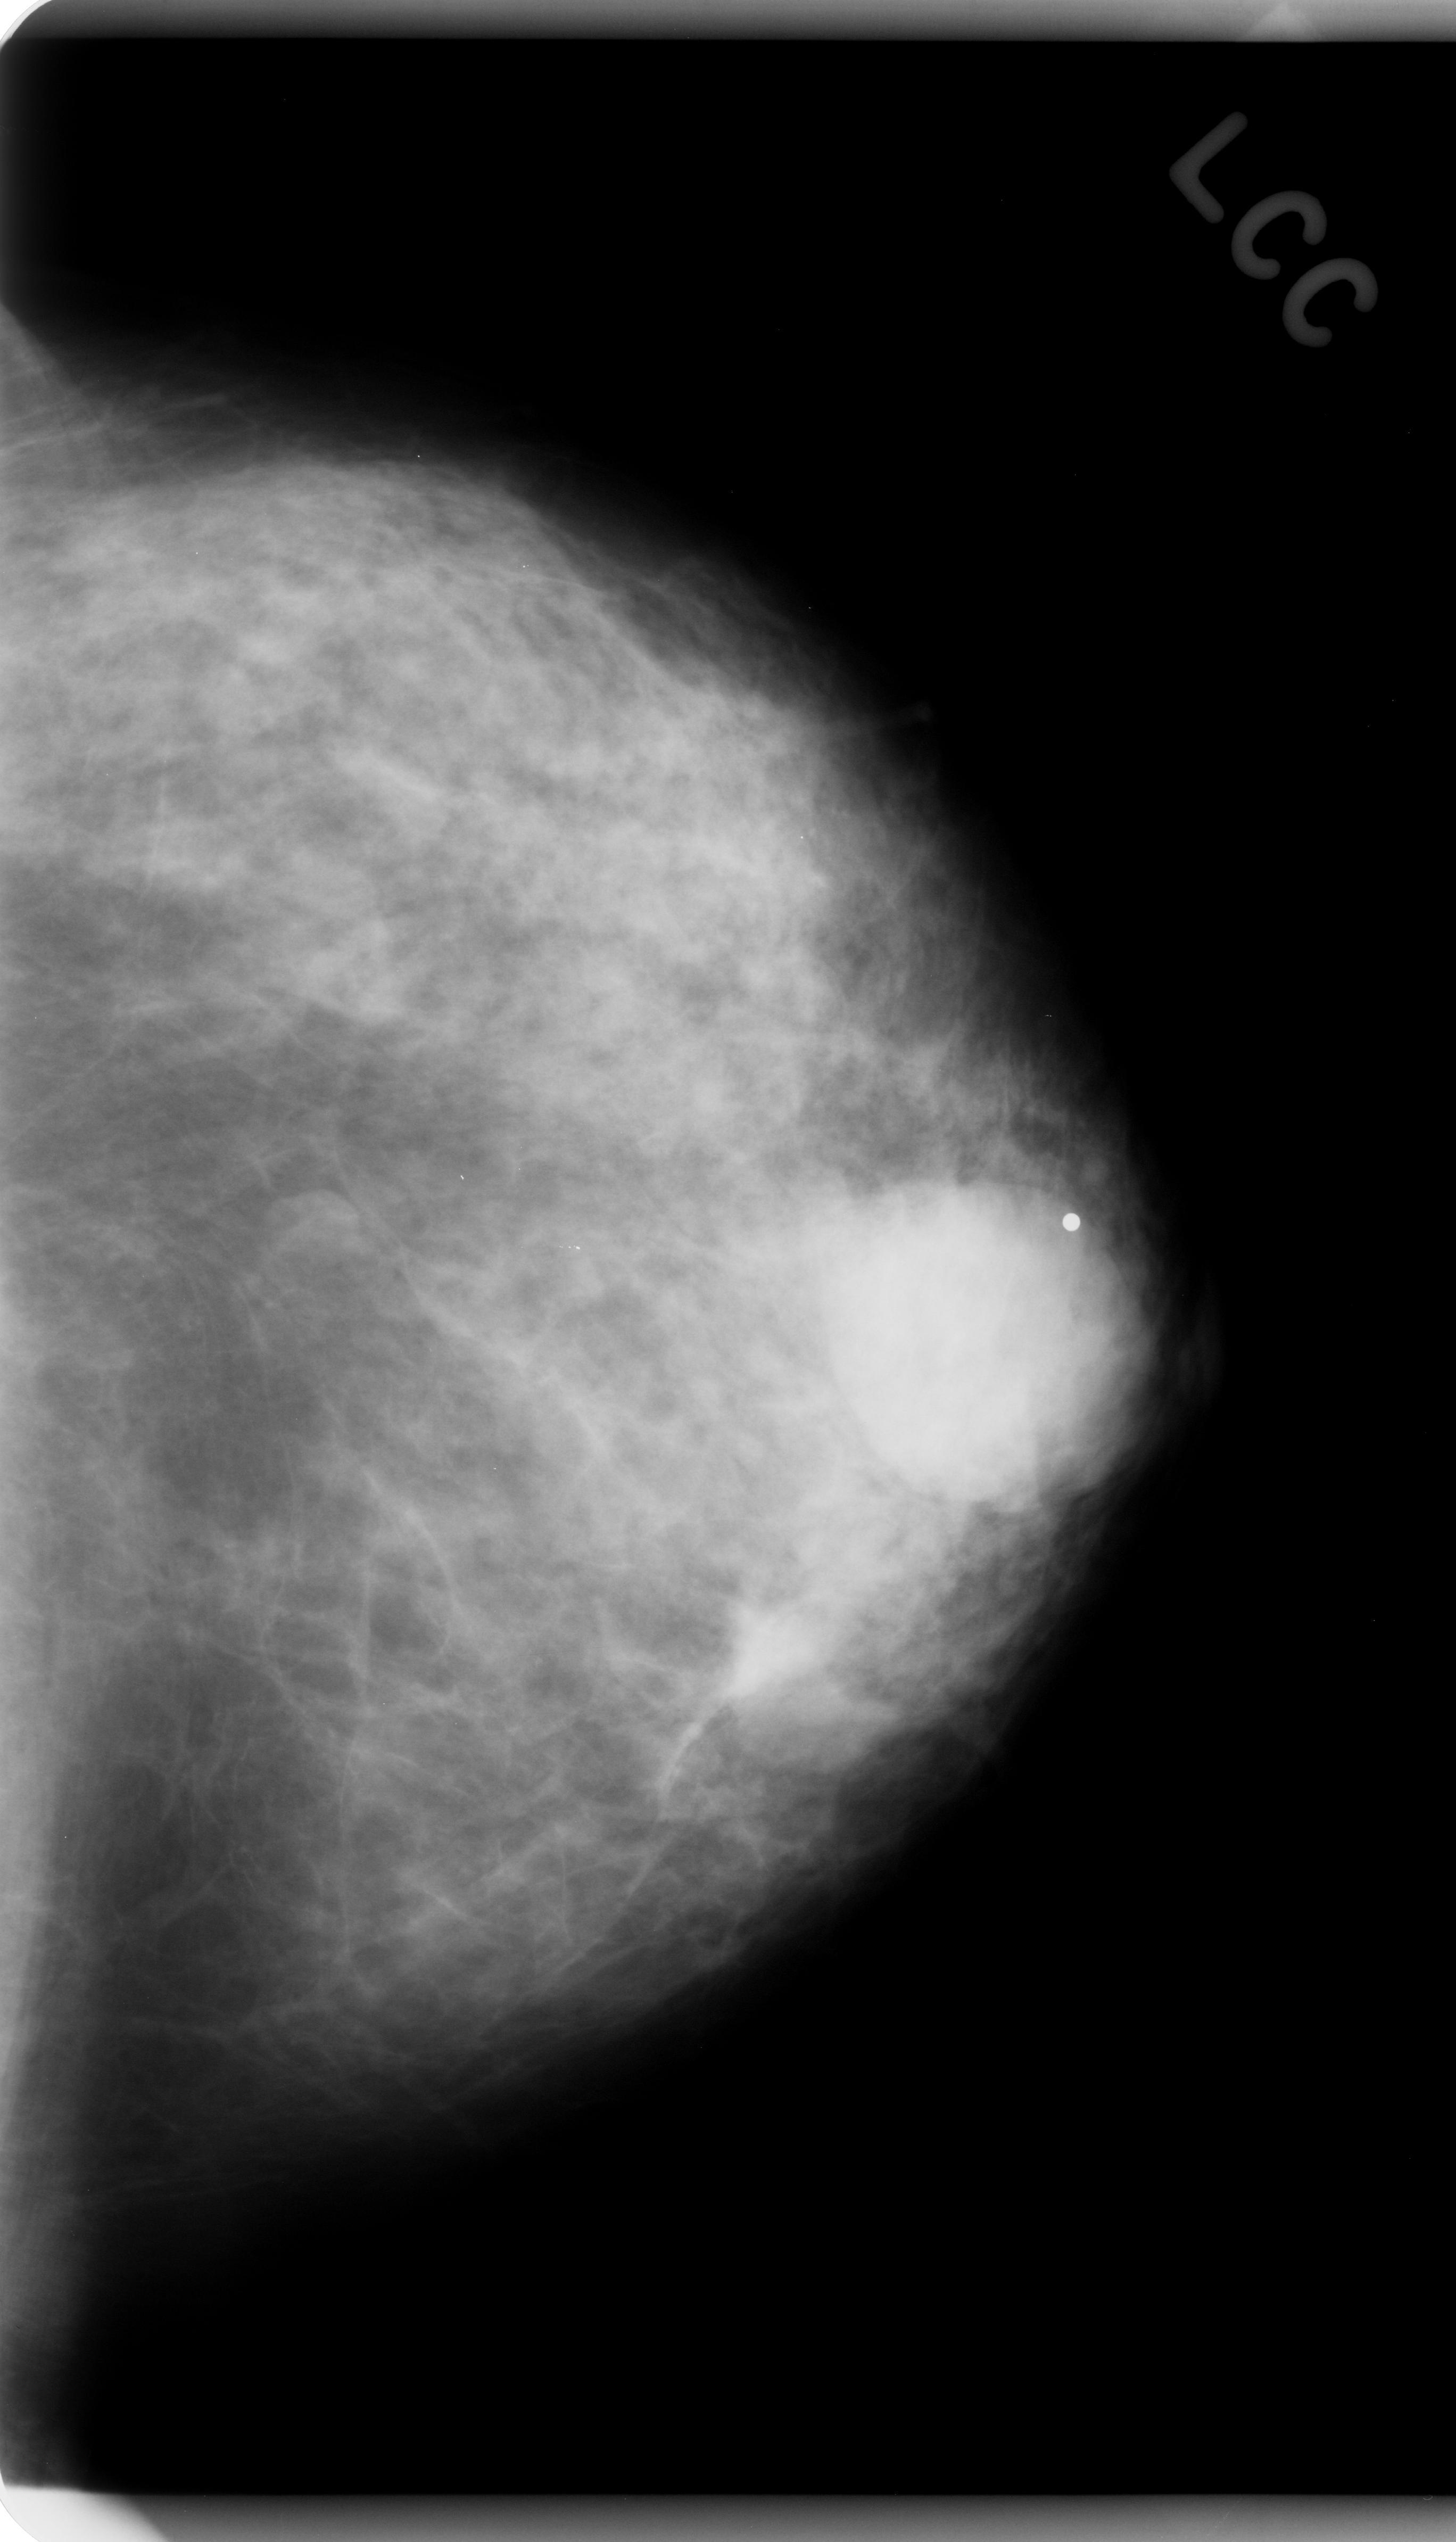
Digitized screen-film mammogram. Left breast. CC view. Breast composition: scattered fibroglandular densities (BI-RADS density category 2 of 4). 1456 × 2542 image matrix.
Marked abnormalities (boxes around the expert regions of interest):
- mass, shape round, margins obscured; BI-RADS assessment category 4; pathology result (as recorded, not read from the image): benign: bounding box [x1, y1, x2, y2] px = [705, 1589, 837, 1730]